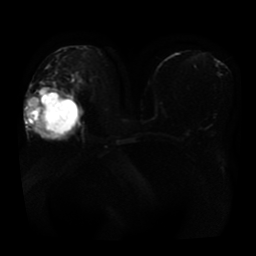
Breast MRI, one axial slice. Slice 24 of 41 in the series (ordered by position). Diffusion-weighted series; image 2 of 4 stored at this slice position (different b-values; order by instance number). 1.5 T. 5 mm slice thickness. 256 × 256 image matrix, field of view 360 × 360 mm. Female patient.
Annotated regions visible in this slice (expert manual segmentation):
- tumour on diffusion-weighted imaging: bounding box (x1, y1, x2, y2) in pixels: (25, 99, 52, 141)